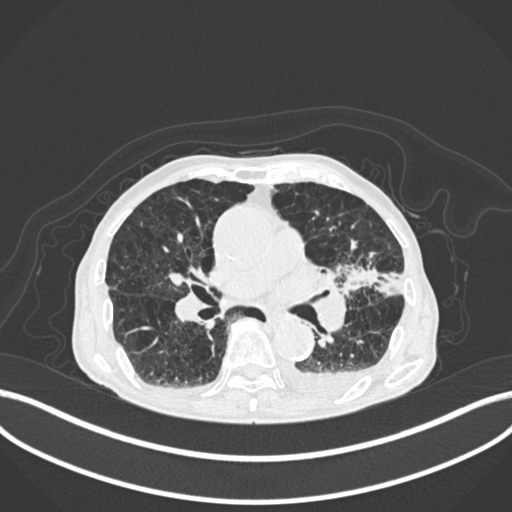
Chest CT, one axial slice; slice 117 of 400 in the series (ordered by position); reconstruction kernel B30f; 120 kVp; lung window (W 1500 / L -600 HU); 1 mm slice thickness; 512 × 512 image matrix, field of view 400 × 400 mm. Male patient, age 90 years or older. Case-level facts recorded for this patient, not image findings: clinical TNM (as recorded): T2b N1 M0.
Annotated regions visible in this slice (bounding box drawn by a radiologist):
- lung tumour (recorded histology: squamous cell carcinoma): box from (x=344, y=264) to (x=384, y=295) px